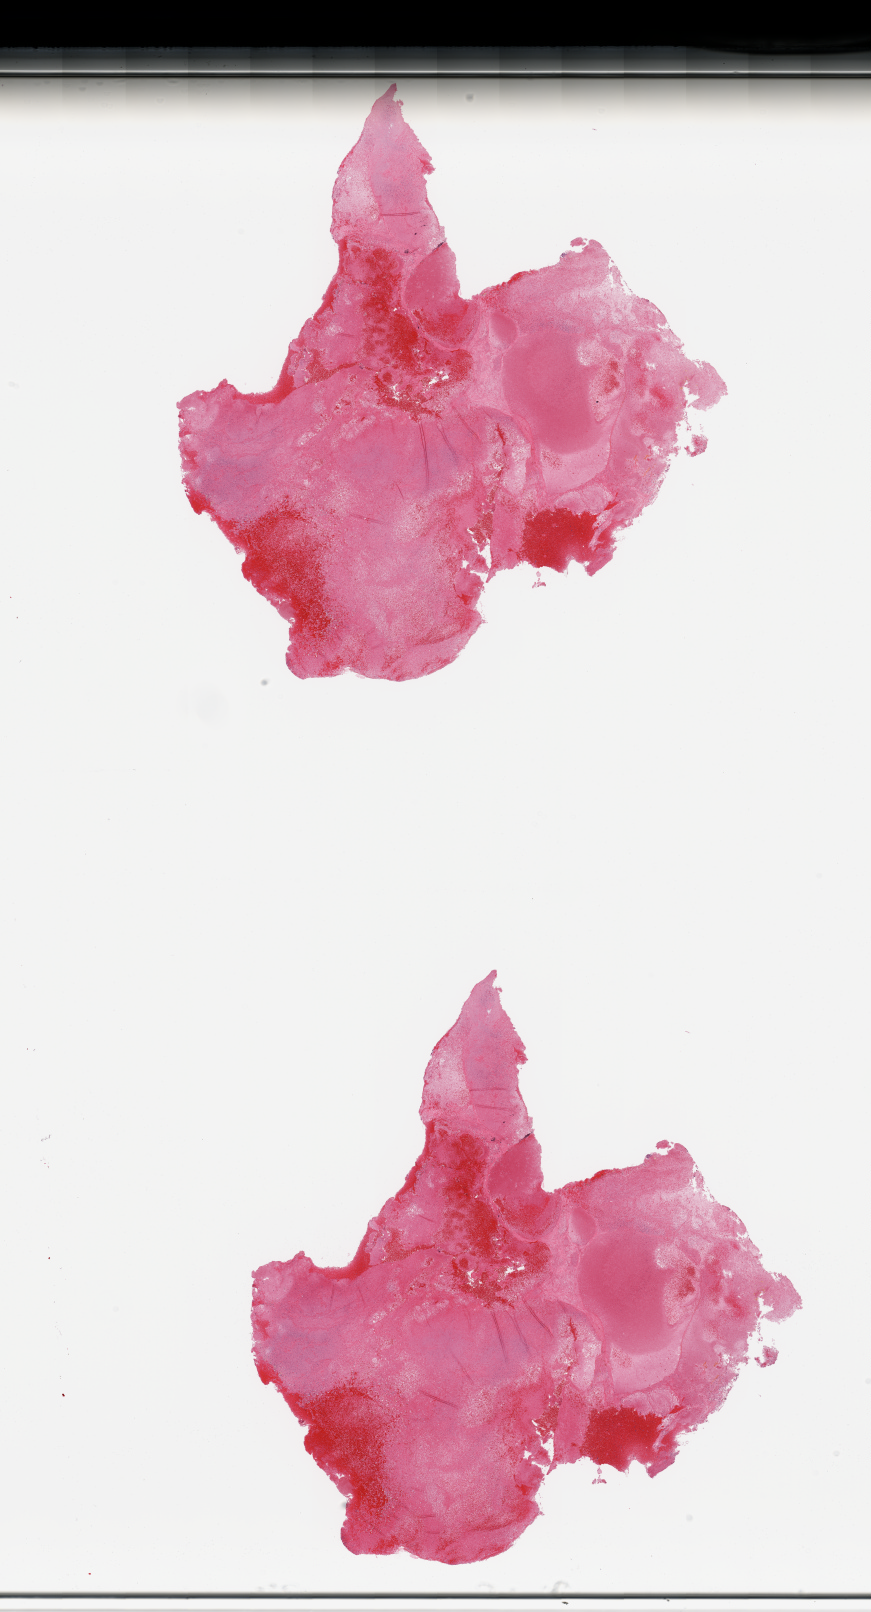
Digitized H&E tissue section (whole slide) — whole scanned area (about 13.8 x 25.5 mm, acquisition: 20x scan) shown as a low-resolution overview, tumour tissue sample, sampled site: kidney. Female, 60 y/o. Histologic grade: G3 (poorly differentiated). Pathologist review of this section (percent, as recorded): tumour nuclei 0%, necrosis 80%.
AJCC pathologic stage: II. Histologic diagnosis: Renal cell carcinoma, NOS.